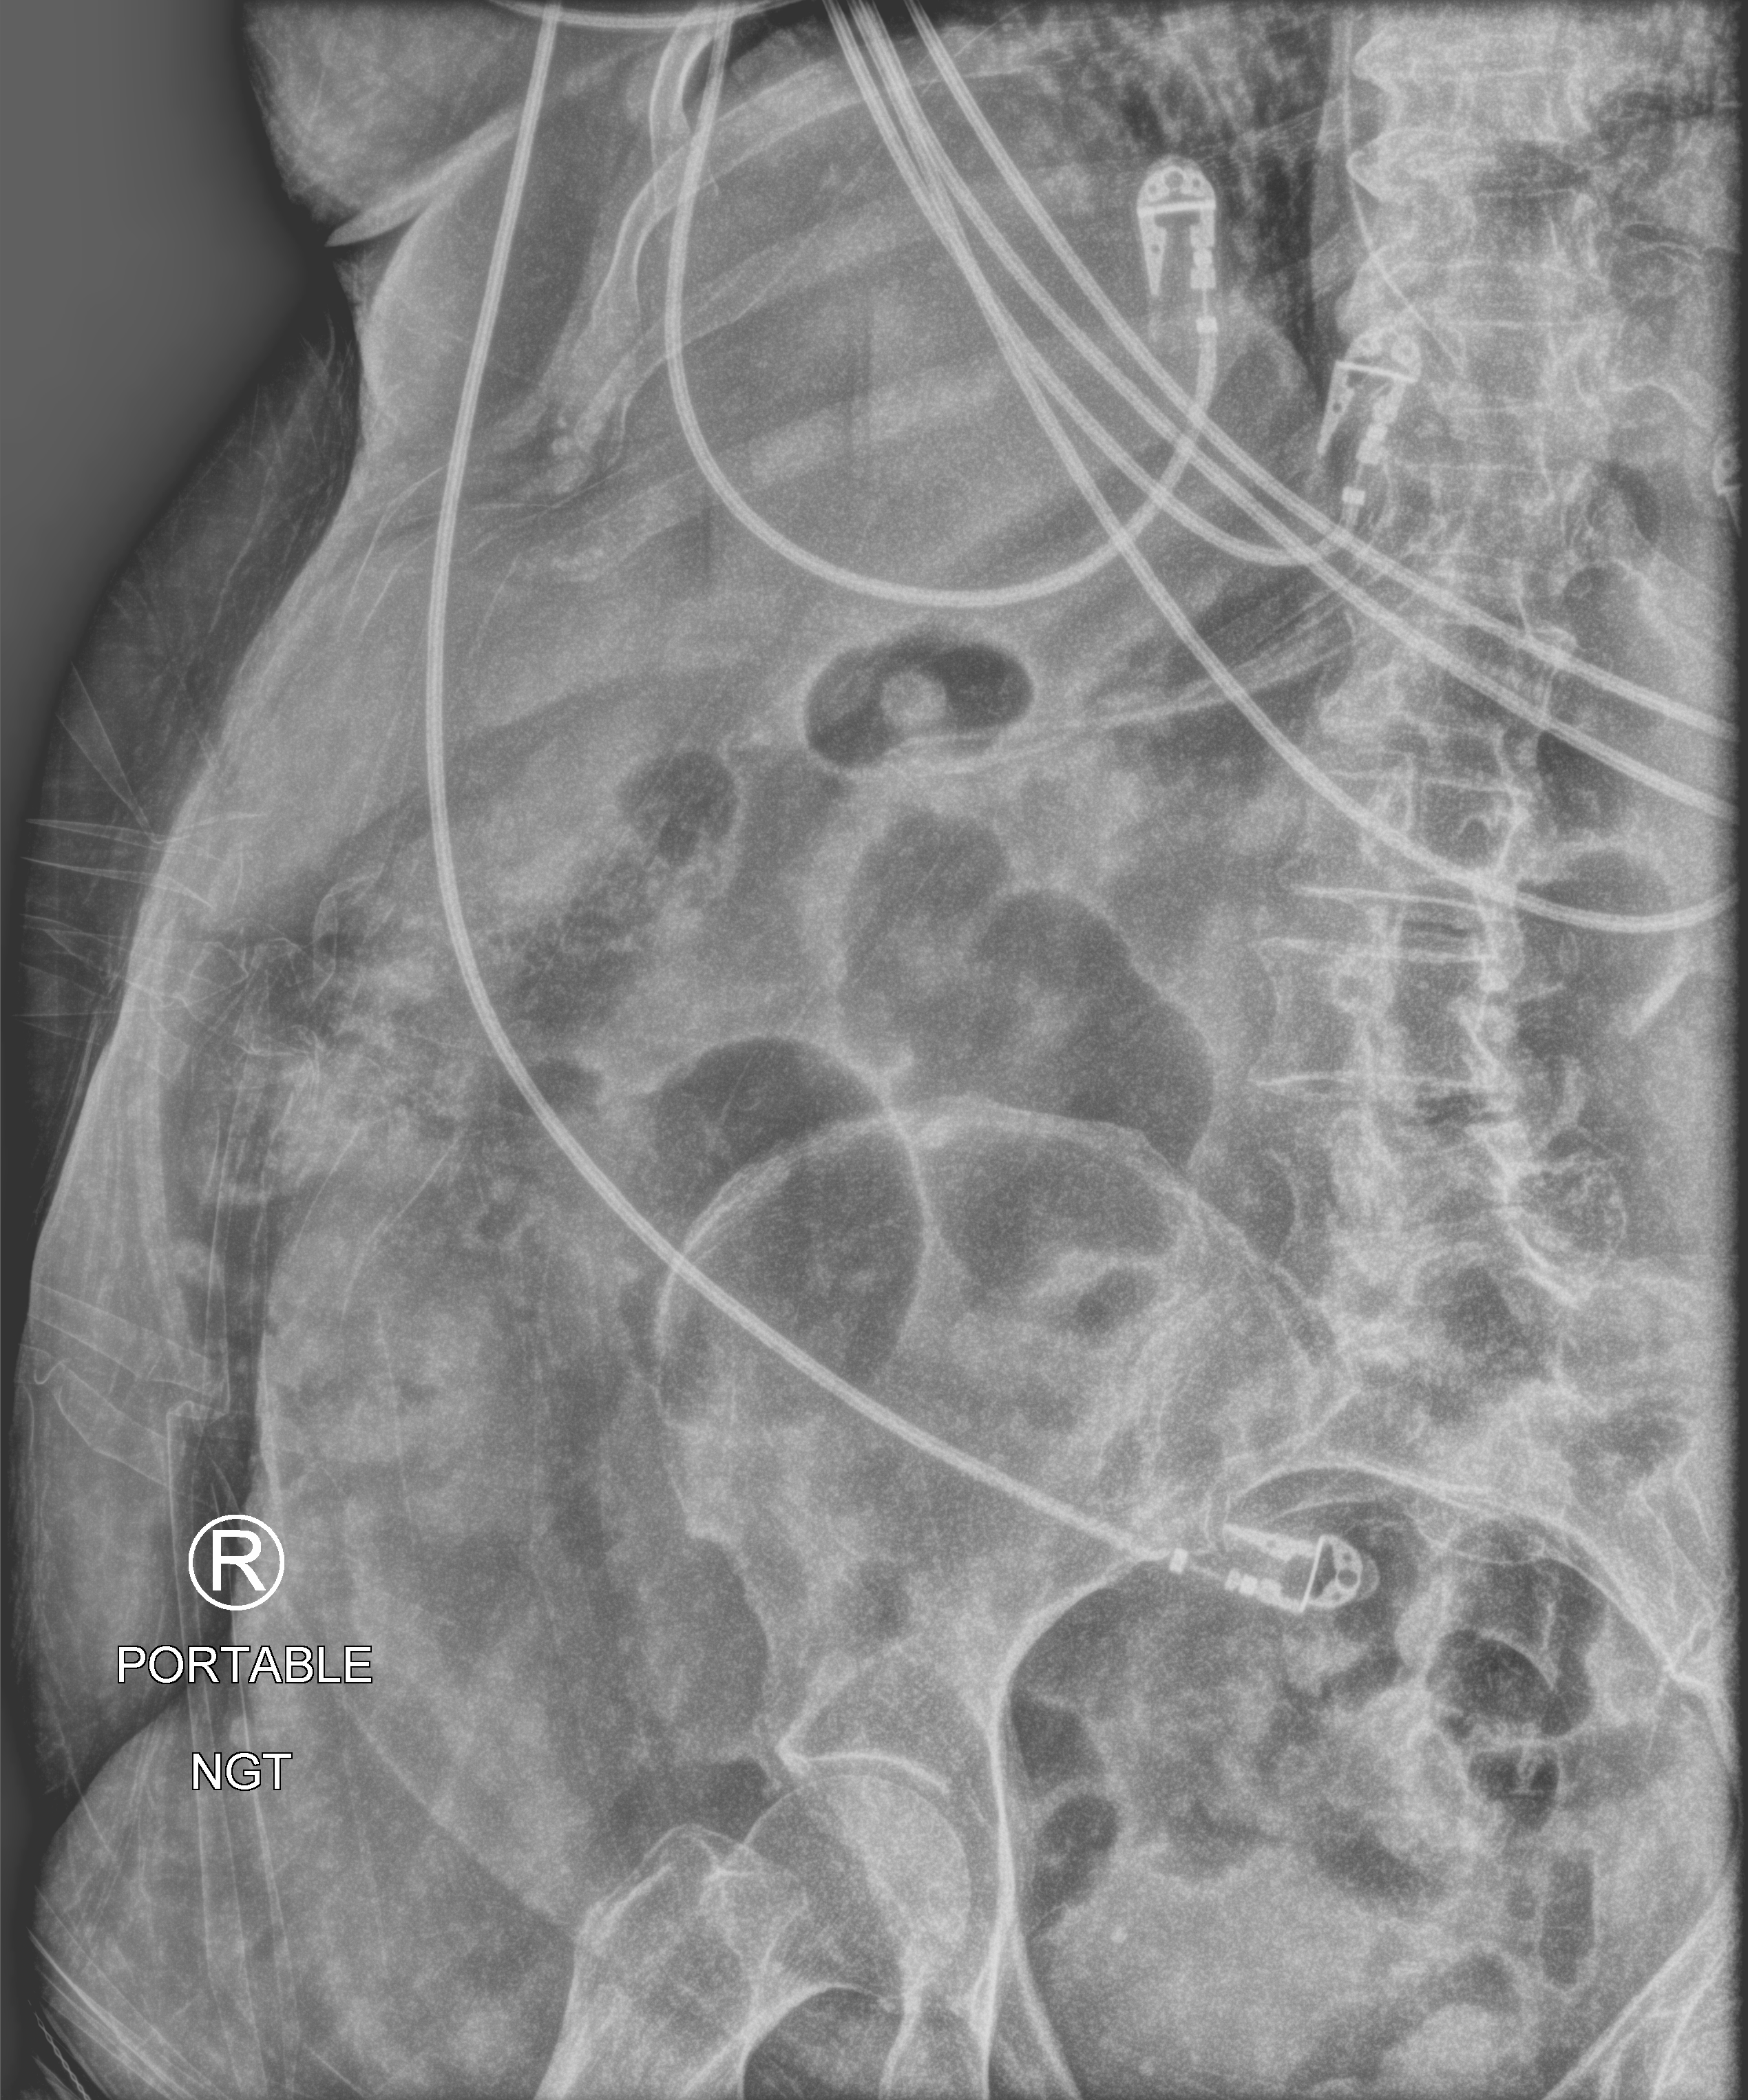
Abdomen X-ray (portable). Patient hospitalised with COVID-19; female, aged 75–90 years.
Admission-level facts for this patient (not findings on this image; timing relative to this image not recorded):
- chronic kidney disease (admission record): no
- mechanically ventilated during this hospital stay: yes